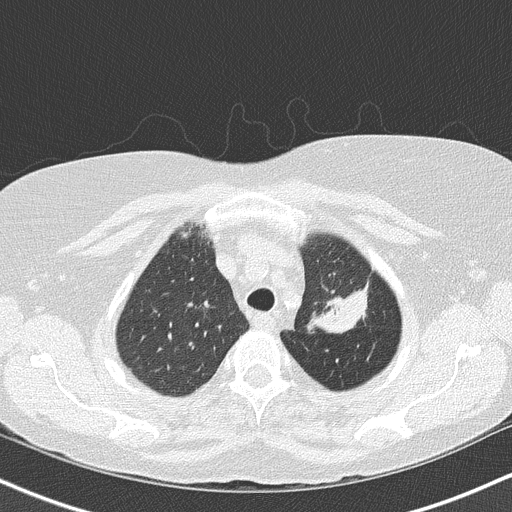
Low-dose screening chest CT, one axial slice; position 123 of 147 along the scan axis; lung window (W 1500 / L -600 HU); 2 mm slice thickness; 512 × 512 image matrix.
Outlined on this slice (expert manual segmentation):
- lesion 1 (tumor, upper lobe of left lung): bounding box [x1, y1, x2, y2] px = [309, 290, 367, 333]